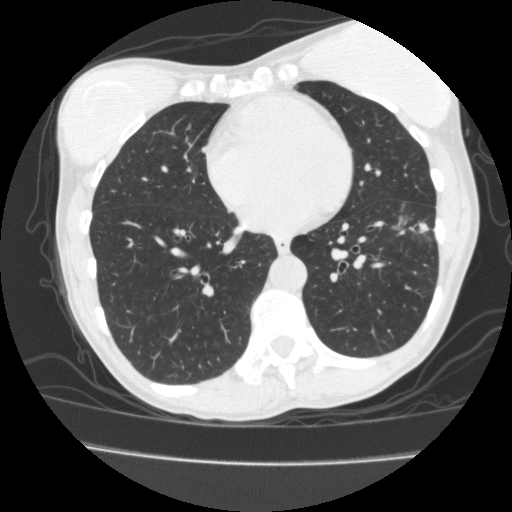
Low-dose screening chest CT, one axial slice. Slice 67 of 171 in the series (ordered by position). Reconstruction kernel FC10. 120 kVp. Lung window (W 1500 / L -600 HU). 2 mm slice thickness. 512 × 512 image matrix, field of view 339 × 339 mm.
Outlined on this slice (manually delineated by an expert):
- lesion 1 (tumor, lower lobe of left lung): box from (x=420, y=224) to (x=427, y=232) px